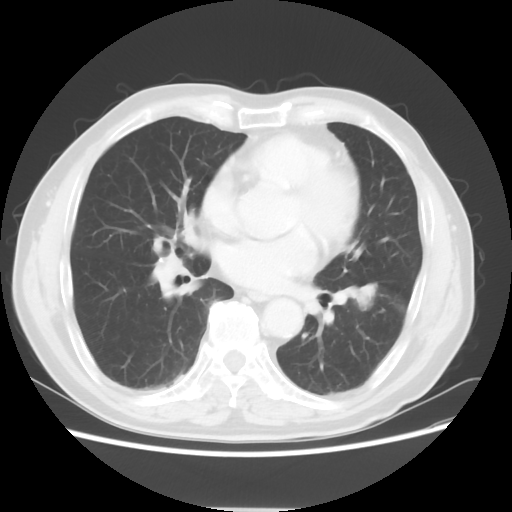
Chest CT, one axial slice. Position 27 of 64 along the scan axis. Reconstruction kernel STANDARD. Lung window (W 1500 / L -600 HU). 5 mm slice thickness. 512 × 512 image matrix, field of view 366 × 366 mm. Male patient, age 71 years. Case-level facts recorded for this patient, not image findings: clinical TNM (as recorded): T1c N1 M0.
Structures marked on this image (rectangle marked by the reading radiologist):
- lung tumour (recorded histology: adenocarcinoma): bounding box (x1, y1, x2, y2) in pixels: (342, 273, 387, 315)